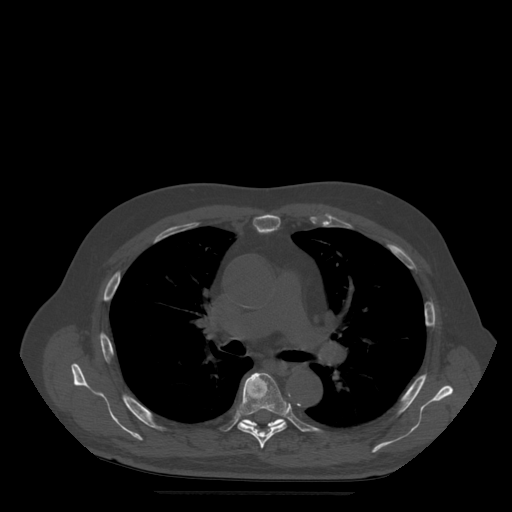
CT including the spine, one axial slice; position 349 of 522 along the scan axis; bone window (W 1800 / L 400 HU); 1.25 mm slice thickness; 512 × 512 image matrix, field of view 420 × 420 mm. Patient age 72 years. From the clinical record (not read from this slice): primary cancer: prostate.
Outlined on this slice (semi-automatic segmentation, software-assisted and operator-edited):
- T6 vertebra: bounding box <238,373,289,449> (left, top, right, bottom; pixels)
- T7 vertebra: <244,419,285,430>